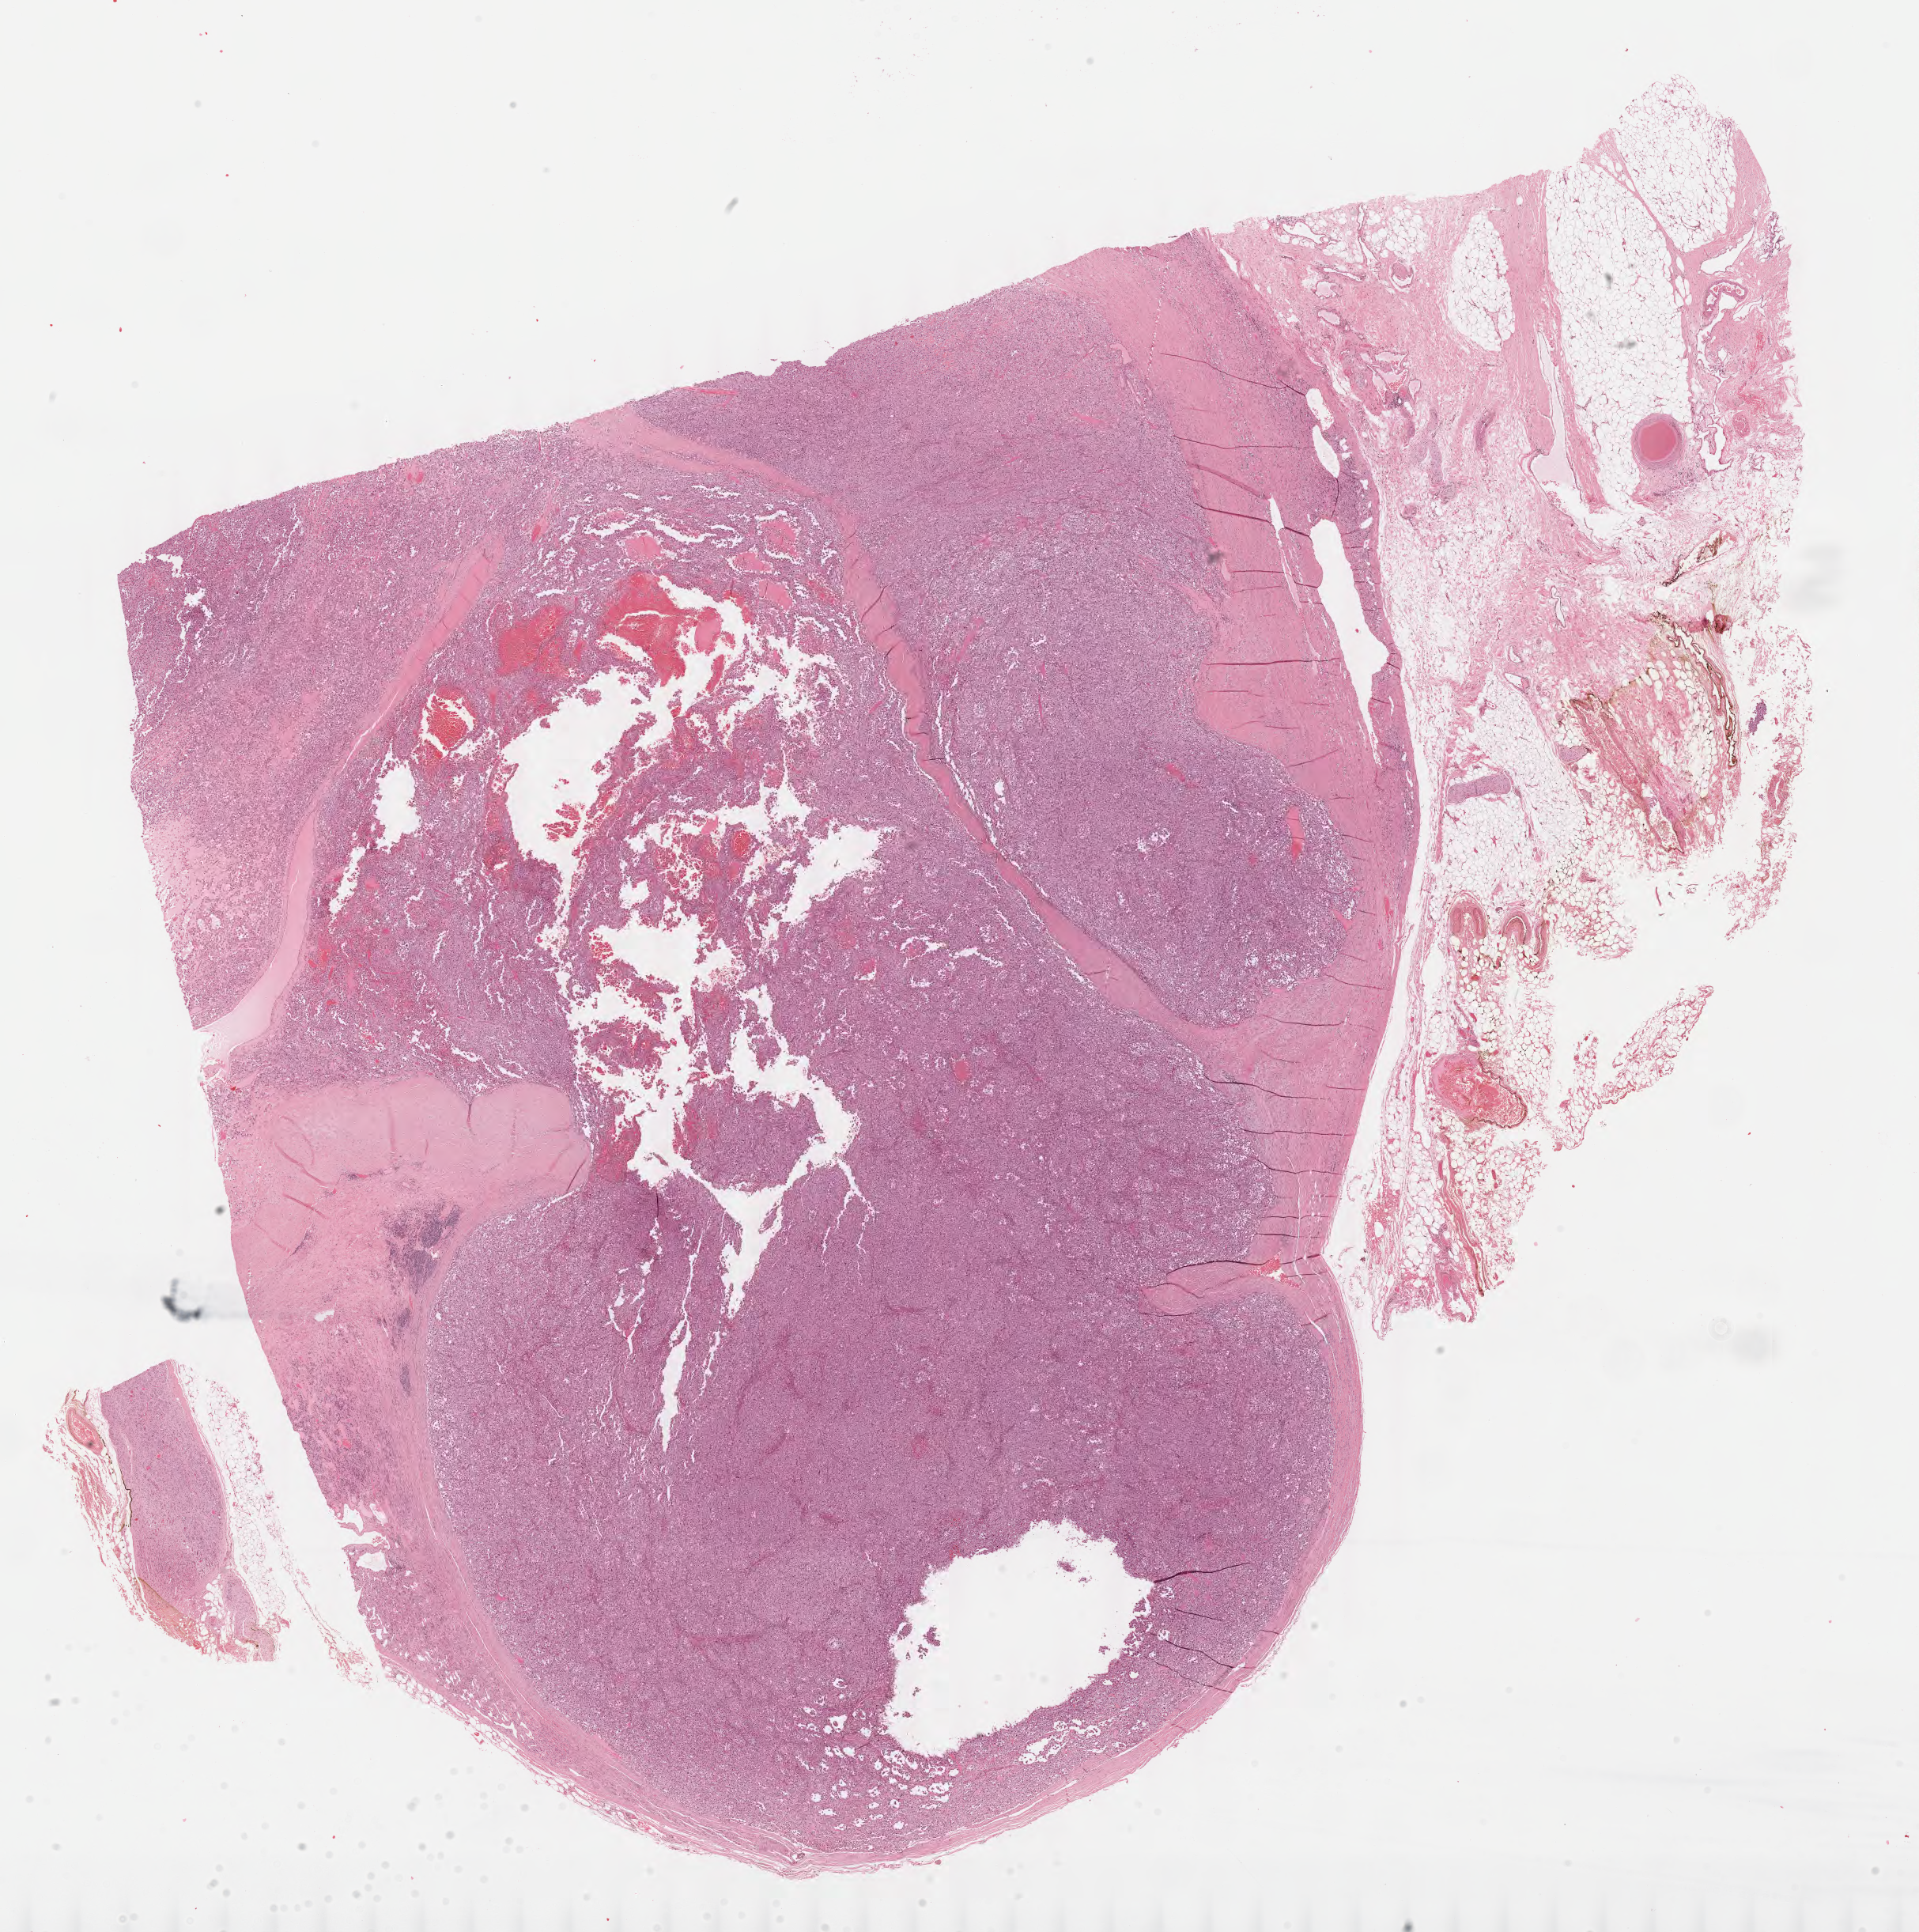
Hematoxylin and eosin (H&E) stained whole-slide image, shown as a low-resolution overview of the whole scanned area (about 19.2 x 19.3 mm); formalin-fixed paraffin-embedded (FFPE) diagnostic section; primary tumour sample from the adrenal cortex. Patient: male, age at initial diagnosis 63 years.
Diagnosis: Adrenal cortical carcinoma (cortex of adrenal gland).